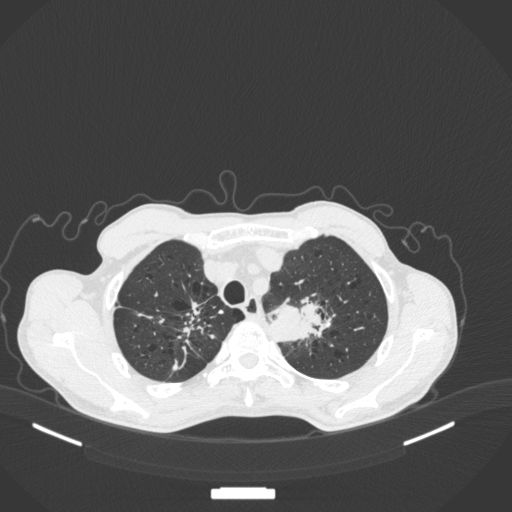
Chest CT, one axial slice; position 356 of 394 along the scan axis; lung window (W 1500 / L -600 HU); 512 × 512 image matrix. Patient: male, 65 years. From the clinical record (not read from this slice): clinical TNM (as recorded): T2b N0 M0.
Outlined on this slice (bounding box drawn by a radiologist):
- lung tumour (recorded histology: adenocarcinoma): bounding box [x1, y1, x2, y2] px = [269, 292, 337, 344]